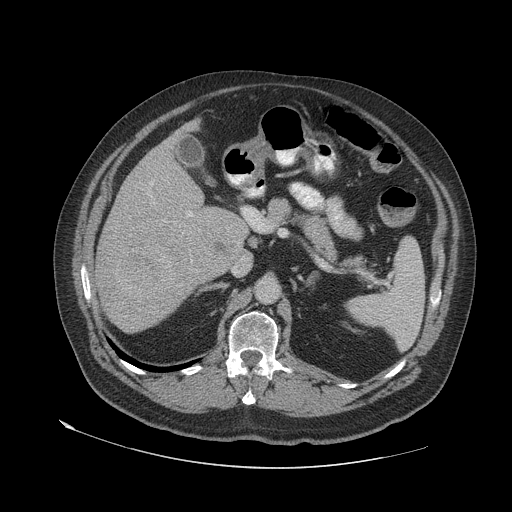
Contrast-enhanced abdominal CT (liver protocol), one axial slice. Position 32 of 79 along the scan axis. Reconstruction kernel STANDARD. 140 kVp. Soft-tissue window (W 400 / L 40 HU). 2.5 mm slice thickness. 512 × 512 image matrix, field of view 480 × 480 mm. Case-level facts recorded for this patient, not image findings: diagnosis: hepatocellular carcinoma (patient treated with transarterial chemoembolisation; whether this scan precedes or follows treatment is not stated here); TNM stage (as recorded): Stage-IVA; Child-Pugh class: A; tumour differentiation: well differentiated; tumour nodularity: multinodular.
Annotated regions visible in this slice (semi-automatically segmented with operator editing):
- liver parenchyma outside the tumour (the mass and vessels are separate outlines, so this box may not span the whole liver): bounding box <94,120,252,332> (left, top, right, bottom; pixels)
- mass: <116,244,172,297>
- liver vessels: <151,183,193,217>